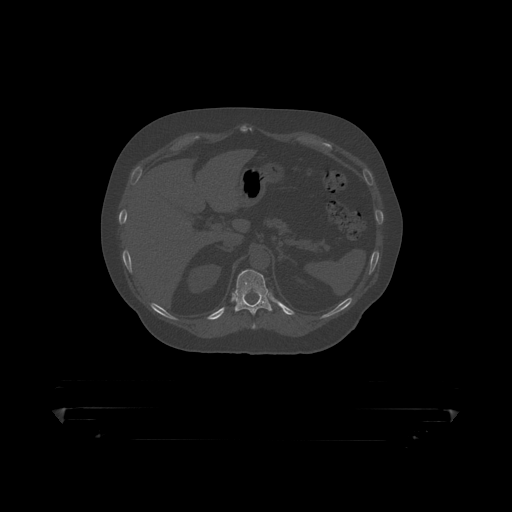
CT including the spine, one axial slice. Position 196 of 390 along the scan axis. 120 kVp. Bone window (W 1800 / L 400 HU). 1.25 mm slice thickness. 512 × 512 image matrix. Male patient, age 60 years. Case-level facts recorded for this patient, not image findings: primary cancer: prostate.
Annotated regions visible in this slice (semi-automatic segmentation, software-assisted and operator-edited):
- T11 vertebra: bounding box (x1, y1, x2, y2) in pixels: (225, 270, 290, 316)